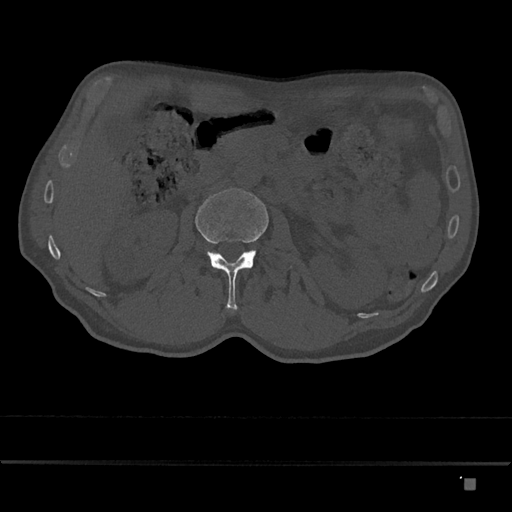
CT including the spine, one axial slice. Position 470 of 797 along the scan axis. Reconstruction kernel Br40s/3. 120 kVp. Bone window (W 1800 / L 400 HU). 0.5 mm slice thickness. 512 × 512 image matrix, field of view 390 × 390 mm. Male patient, age 72 years. Case-level facts recorded for this patient, not image findings: primary cancer: prostate.
Structures marked on this image (semi-automatic segmentation, software-assisted and operator-edited):
- L2 vertebra: bounding box <195,188,269,310> (left, top, right, bottom; pixels)